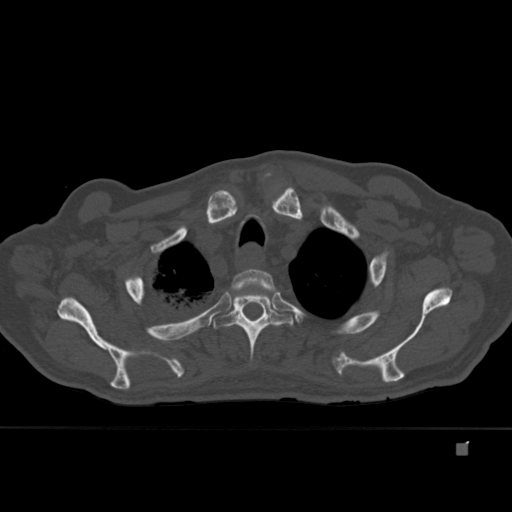
CT including the spine, one axial slice; position 337 of 451 along the scan axis; bone window (W 1800 / L 400 HU); 1.5 mm slice thickness; 512 × 512 image matrix, field of view 378 × 378 mm. Male patient, age 75 years. From the clinical record (not read from this slice): primary cancer: prostate.
Structures marked on this image (semi-automatically segmented with operator editing):
- T2 vertebra: box from (x=226, y=269) to (x=281, y=309) px
- T3 vertebra: (x=211, y=287)–(x=294, y=359)